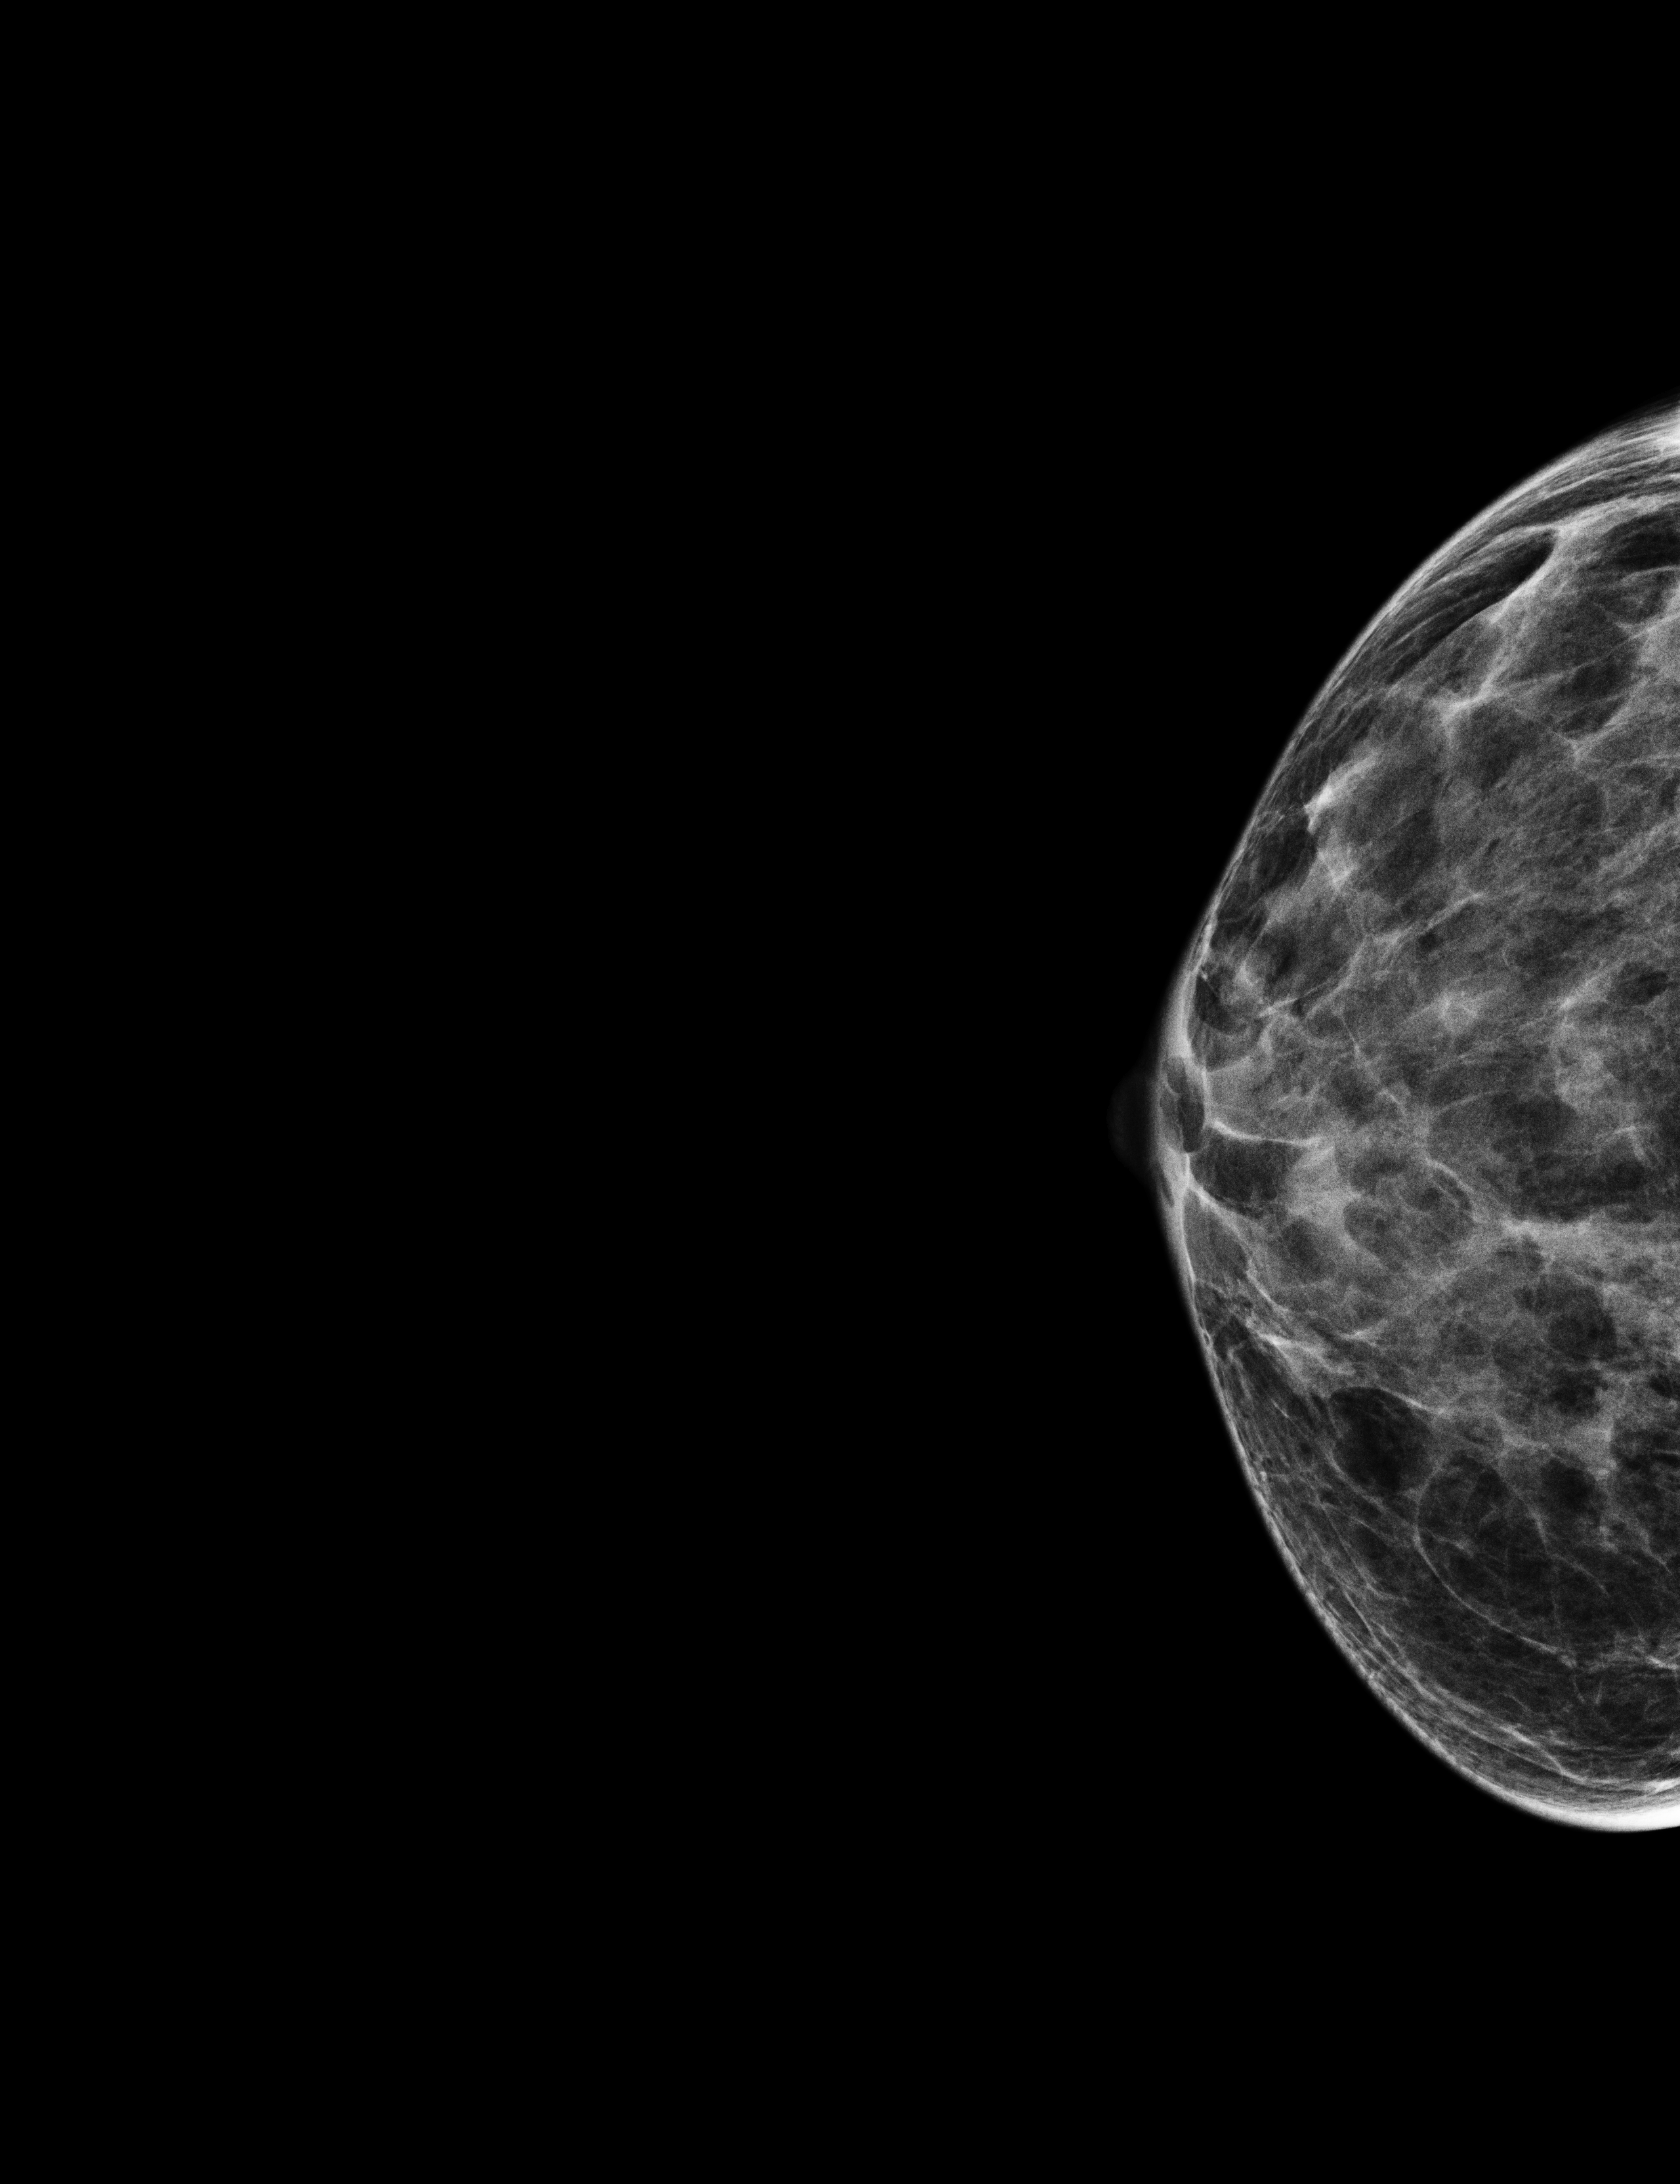
Digital mammogram (FFDM); right breast; CC view; screening examination; compressed breast thickness 19 mm. Female patient, age 68 years.
- BI-RADS breast density category at the screening exam (both breasts, scale 1–4): 4
- final BI-RADS assessment for this screening round (tomosynthesis exam, both breasts): category 1
- recall: no recall after this screen